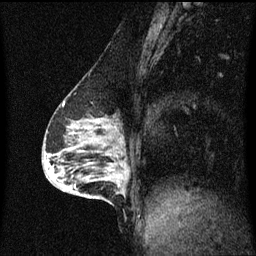
Breast MRI (dynamic contrast-enhanced), one sagittal slice; slice 27 of 60 in the series (ordered by position); dynamic contrast-enhanced series, image 2 of 3 at this slice position (ordered by acquisition); 1.5 T; TE 4.2 ms, TR 8.4 ms; 256 × 256 image matrix, field of view 200 × 200 mm. Patient: female, 64 years.
Outlined on this slice (semi-automatically segmented with operator editing):
- analysis volume of interest (the breast-tissue region the enhancement analysis was run in; not a lesion): bounding box (x1, y1, x2, y2) in pixels: (90, 164, 129, 203)
- tumour enhancement mask (voxels above the 70 % enhancement threshold inside the analysis volume of interest): (108, 168, 129, 193)